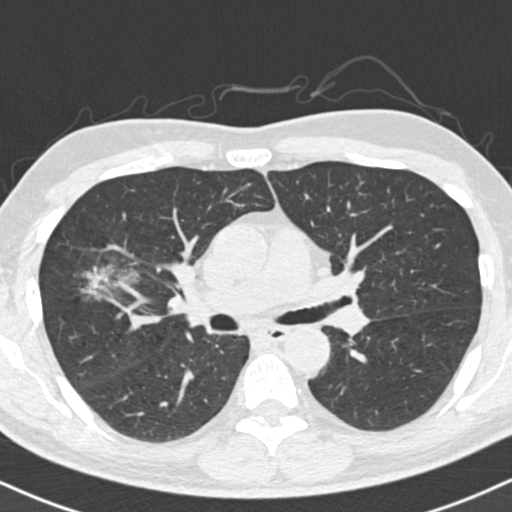
Low-dose screening chest CT, axial slice. First (baseline) screen. Lung window (W 1500 / L -600 HU). 2 mm slice thickness. 512 × 512 image matrix, field of view 322 × 322 mm. Male, age 56 years at enrolment. Former smoker at enrolment.
Expert-annotated lung lesion, bounding box <58,252,148,318> (left, top, right, bottom; pixels). Screening reader's record for this exam: no non-calcified nodule ≥4 mm recorded. Later outcome: lung cancer diagnosed 392 days after this screen (after the second annual screen) — bronchiolo-alveolar adenocarcinoma, NOS, right upper lobe, well differentiated (G1), stage IIB (AJCC 6th edition), 30 mm at pathology.